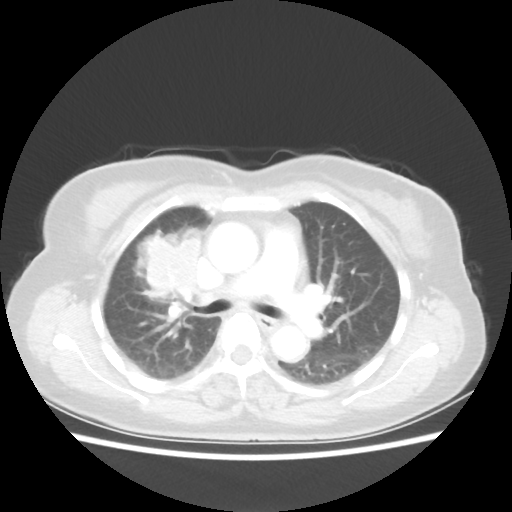
Chest CT, one axial slice; slice 34 of 55 in the series (ordered by position); reconstruction kernel STANDARD; 80 kVp; lung window (W 1500 / L -600 HU); 512 × 512 image matrix, field of view 337 × 337 mm. Patient: female, 62 years. Case-level facts recorded for this patient, not image findings: clinical TNM (as recorded): T4 N3 M0.
Outlined on this slice (rectangle marked by the reading radiologist):
- lung tumour (recorded histology: squamous cell carcinoma): bounding box [x1, y1, x2, y2] px = [135, 224, 204, 312]